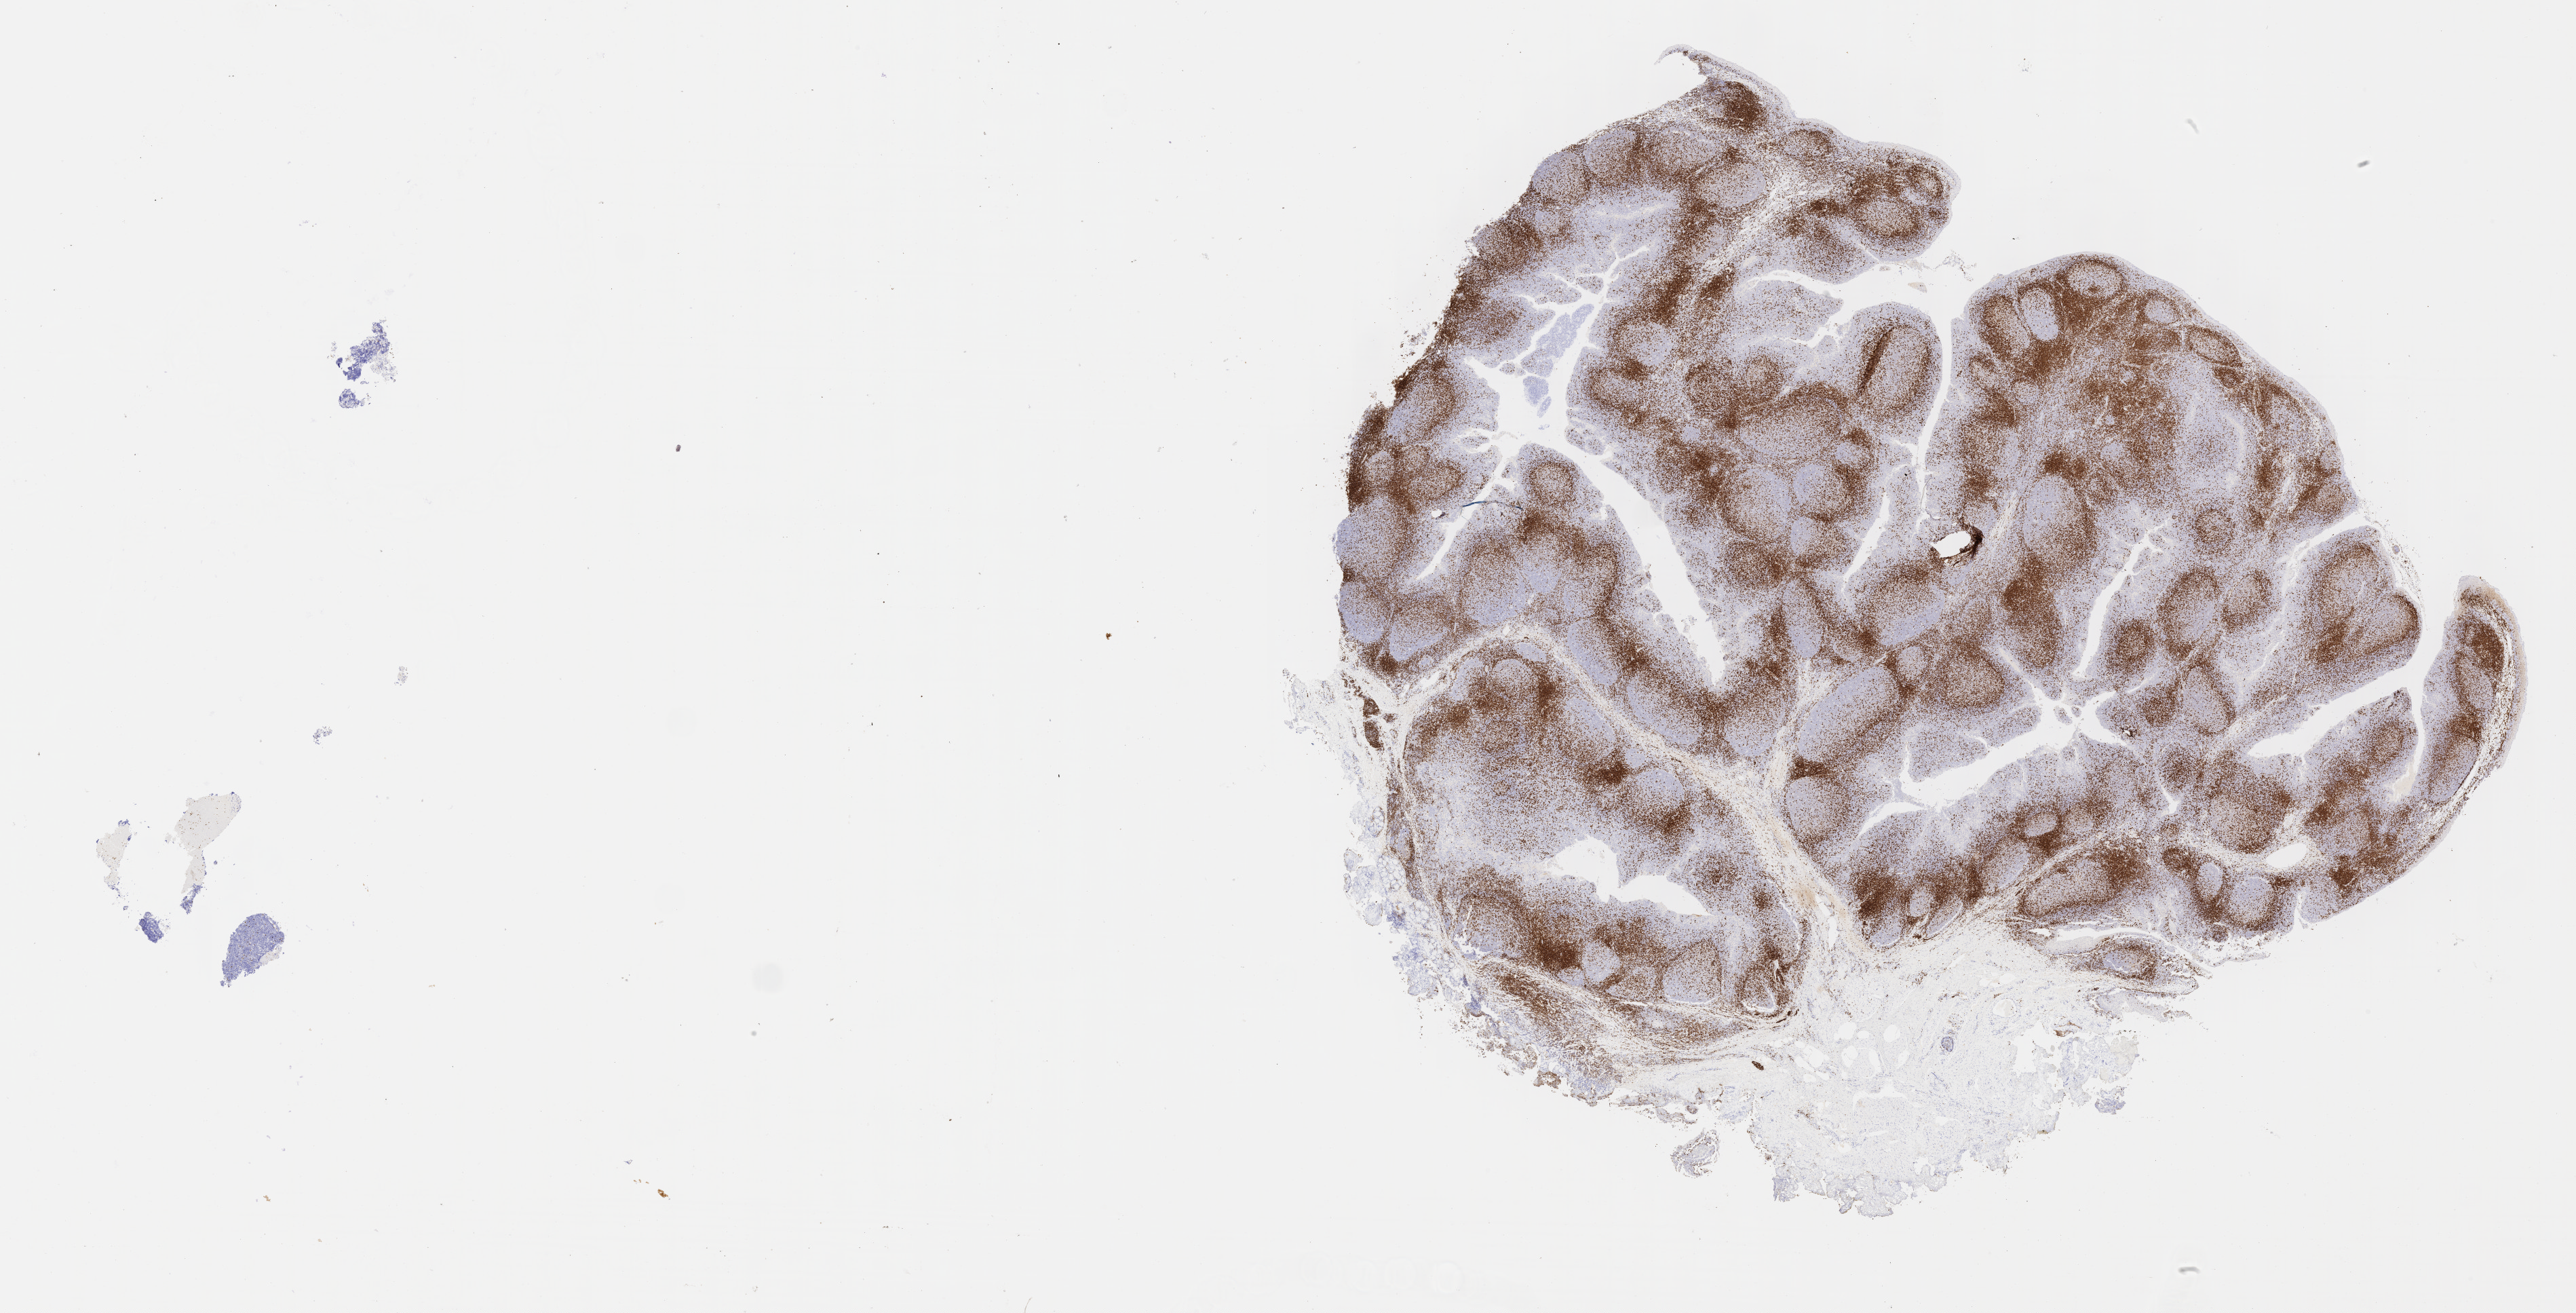
Whole-slide image, immunohistochemical stain for CD3 — a low-resolution overview of the entire scanned area, about 30.7 x 15.6 mm; specimen: tumor tissue; anatomic site: abdominal lymph node. Male patient; age at initial diagnosis 5 years.
Histologic diagnosis: Diffuse large B-cell lymphoma, NOS.